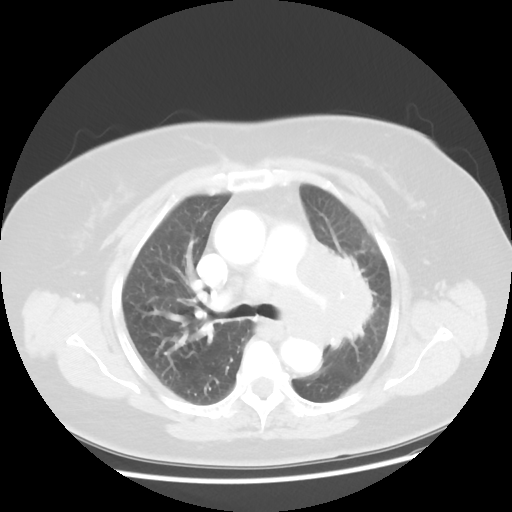
Chest CT, one axial slice; position 30 of 49 along the scan axis; 120 kVp; lung window (W 1500 / L -600 HU); 5 mm slice thickness; 512 × 512 image matrix, field of view 374 × 374 mm. Patient: female, 58 years. From the clinical record (not read from this slice): clinical TNM (as recorded): T4 N3 M0; histopathological grade: G3.
Structures marked on this image (rectangle marked by the reading radiologist):
- lung tumour (recorded histology: small cell carcinoma): box from (x=273, y=227) to (x=376, y=367) px